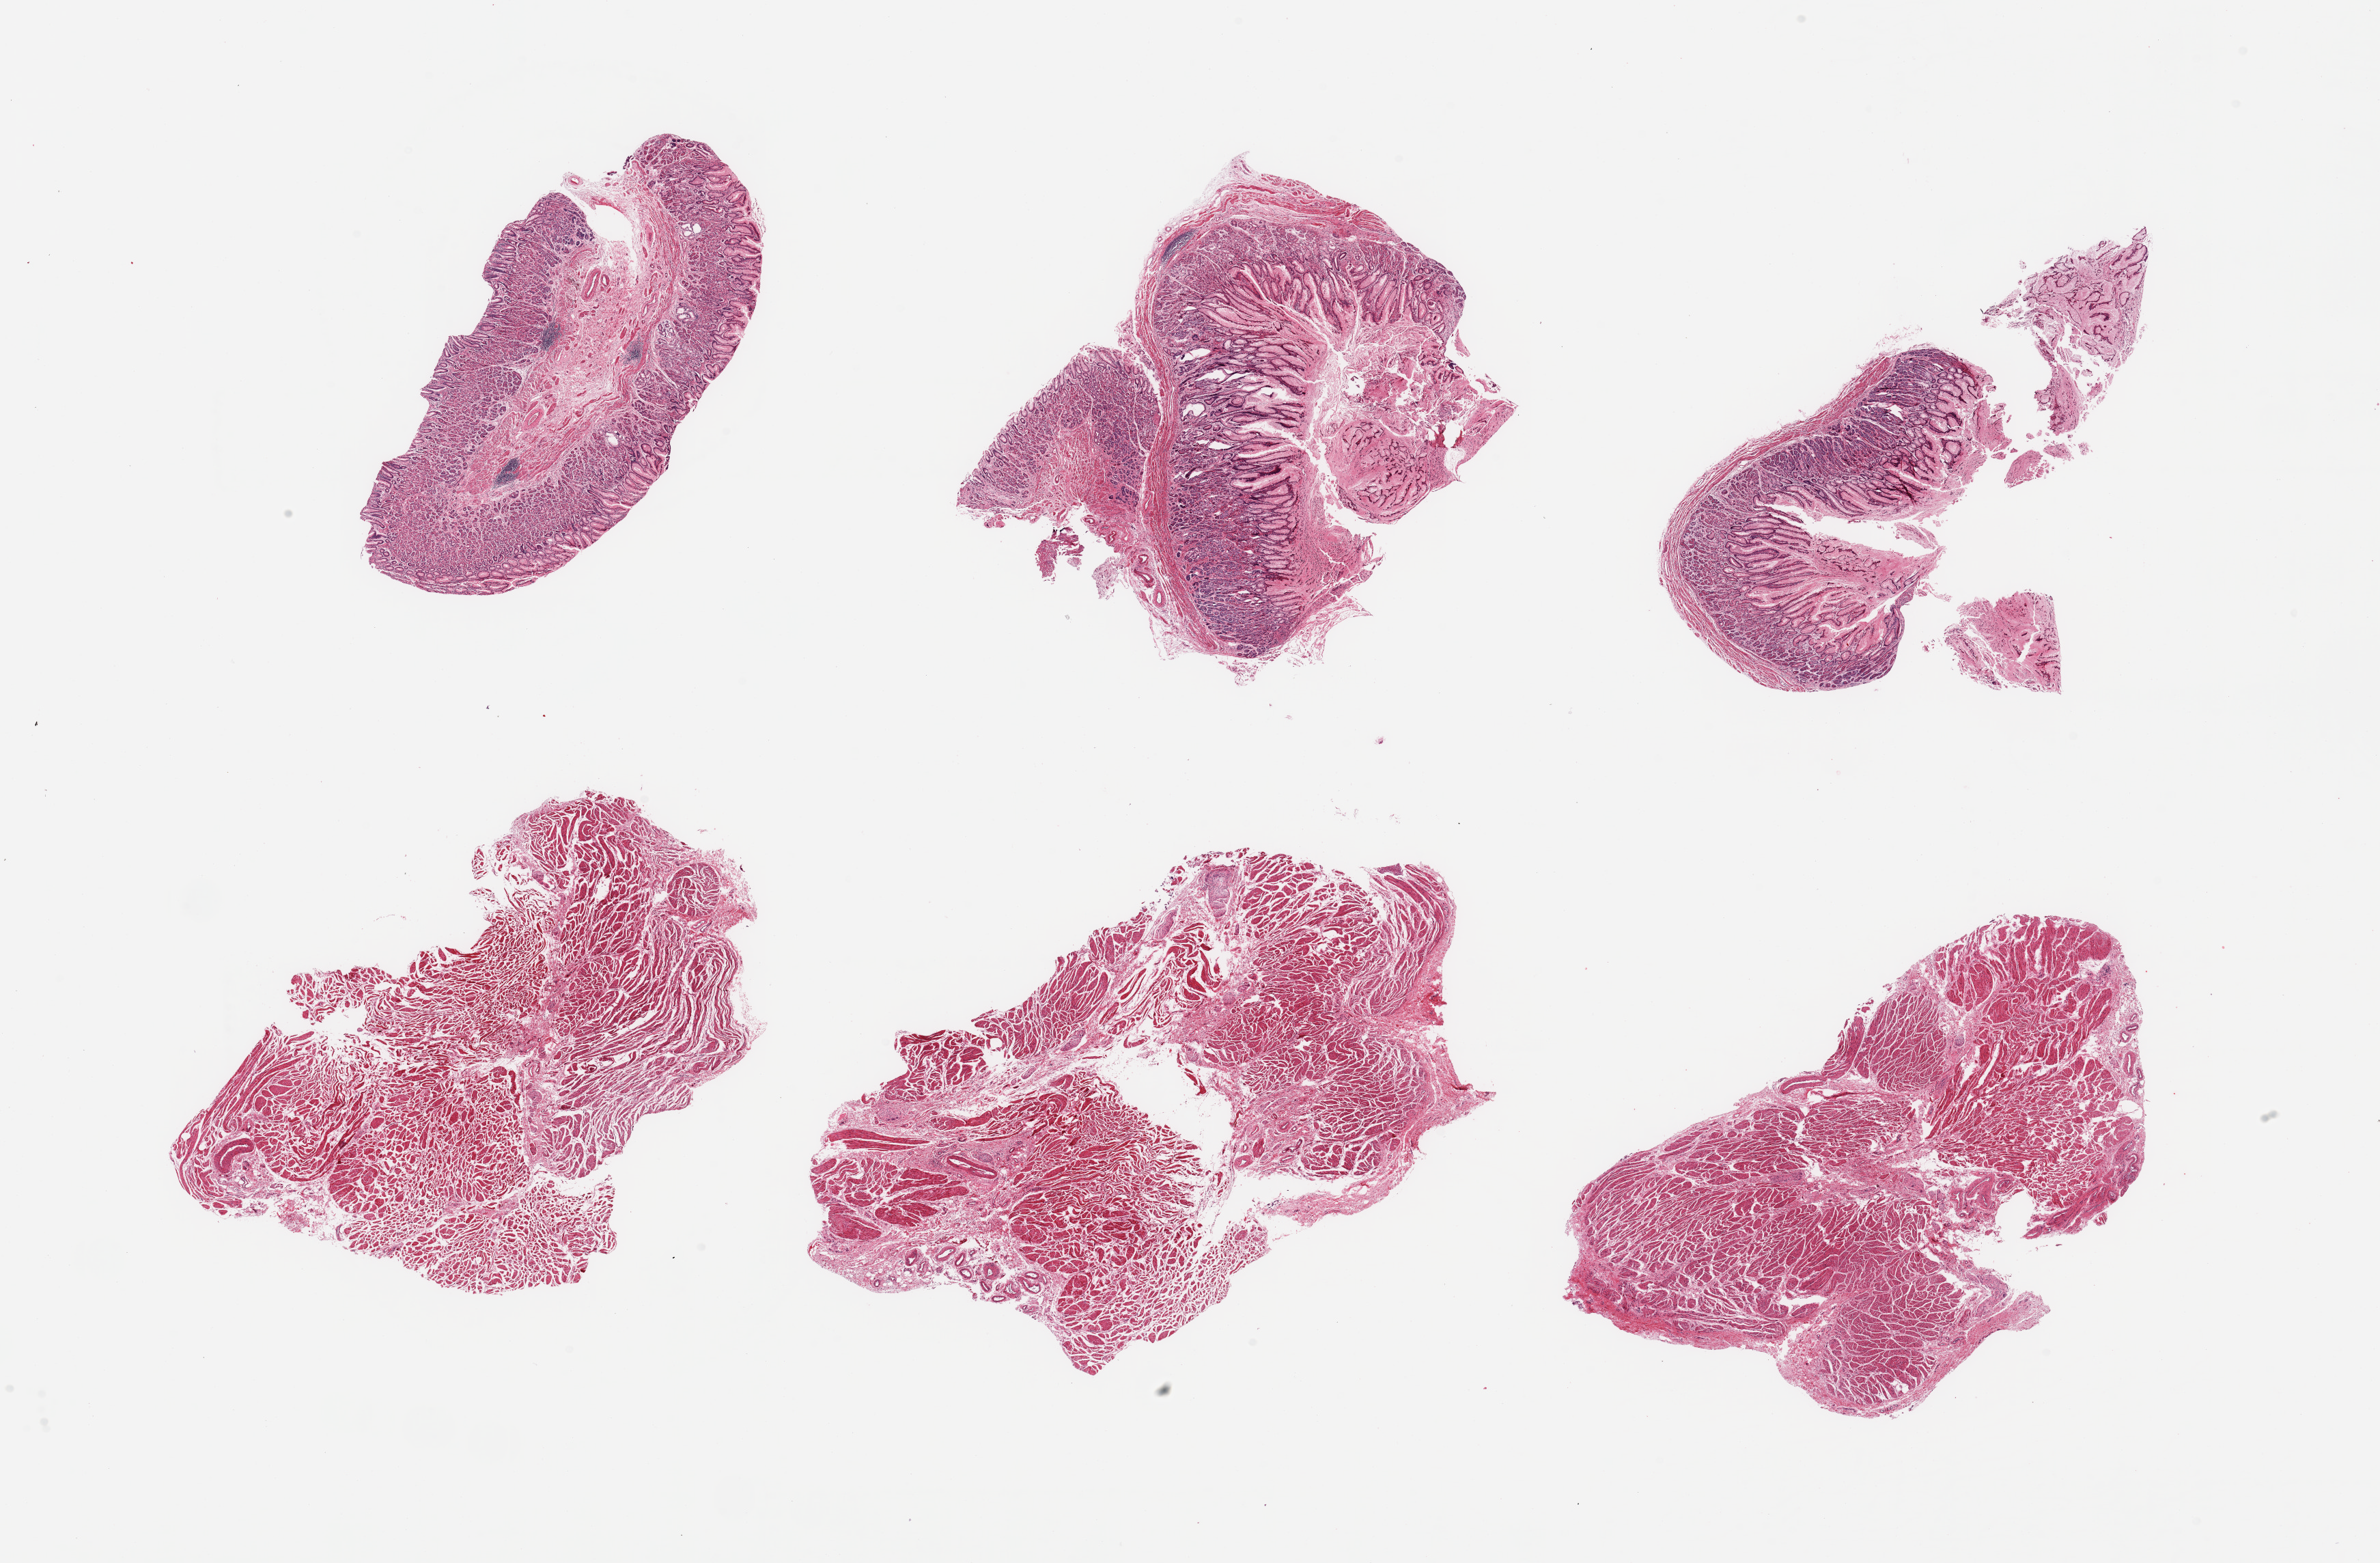
Whole-slide image, H&E stain — a low-resolution overview of the entire scanned area, about 27.6 x 18.1 mm. PAXgene-fixed, paraffin-embedded tissue. Section of gastroesophageal junction (target tissue). Tissue donor sample. Male donor.
* reviewer comment on this tissue sample: 6 pieces; 3 of 6 pieces are gastric mucosa